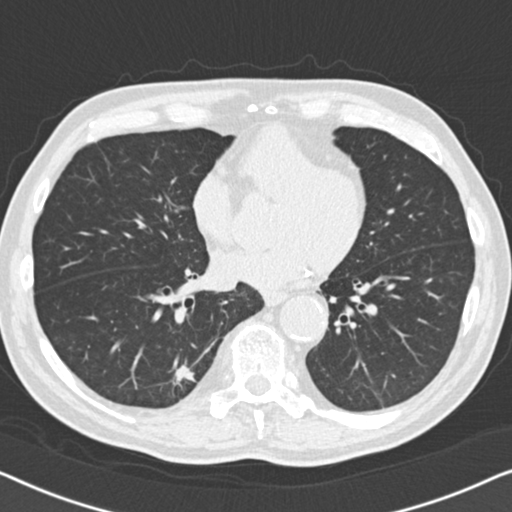
Axial slice from a low-dose chest CT screening exam, second annual screen, lung window (W 1500 / L -600 HU), 2 mm slice thickness, 120 kVp, slice 107 of 164 in the series, 512 × 512 image matrix, field of view 330 × 330 mm. Male, age 74 years at enrolment. Current smoker at enrolment.
Lesion marked by an expert reader, bounding box <146,340,218,410> (left, top, right, bottom; pixels). The screening reader recorded 5 non-calcified nodules or masses ≥4 mm on this exam; which of them this box marks is not recorded. Later outcome: lung cancer diagnosed 55 days after this screen — bronchiolo-alveolar adenocarcinoma, NOS, right lower lobe, moderately differentiated (G2), stage IA (AJCC 6th edition), 16 mm at pathology.